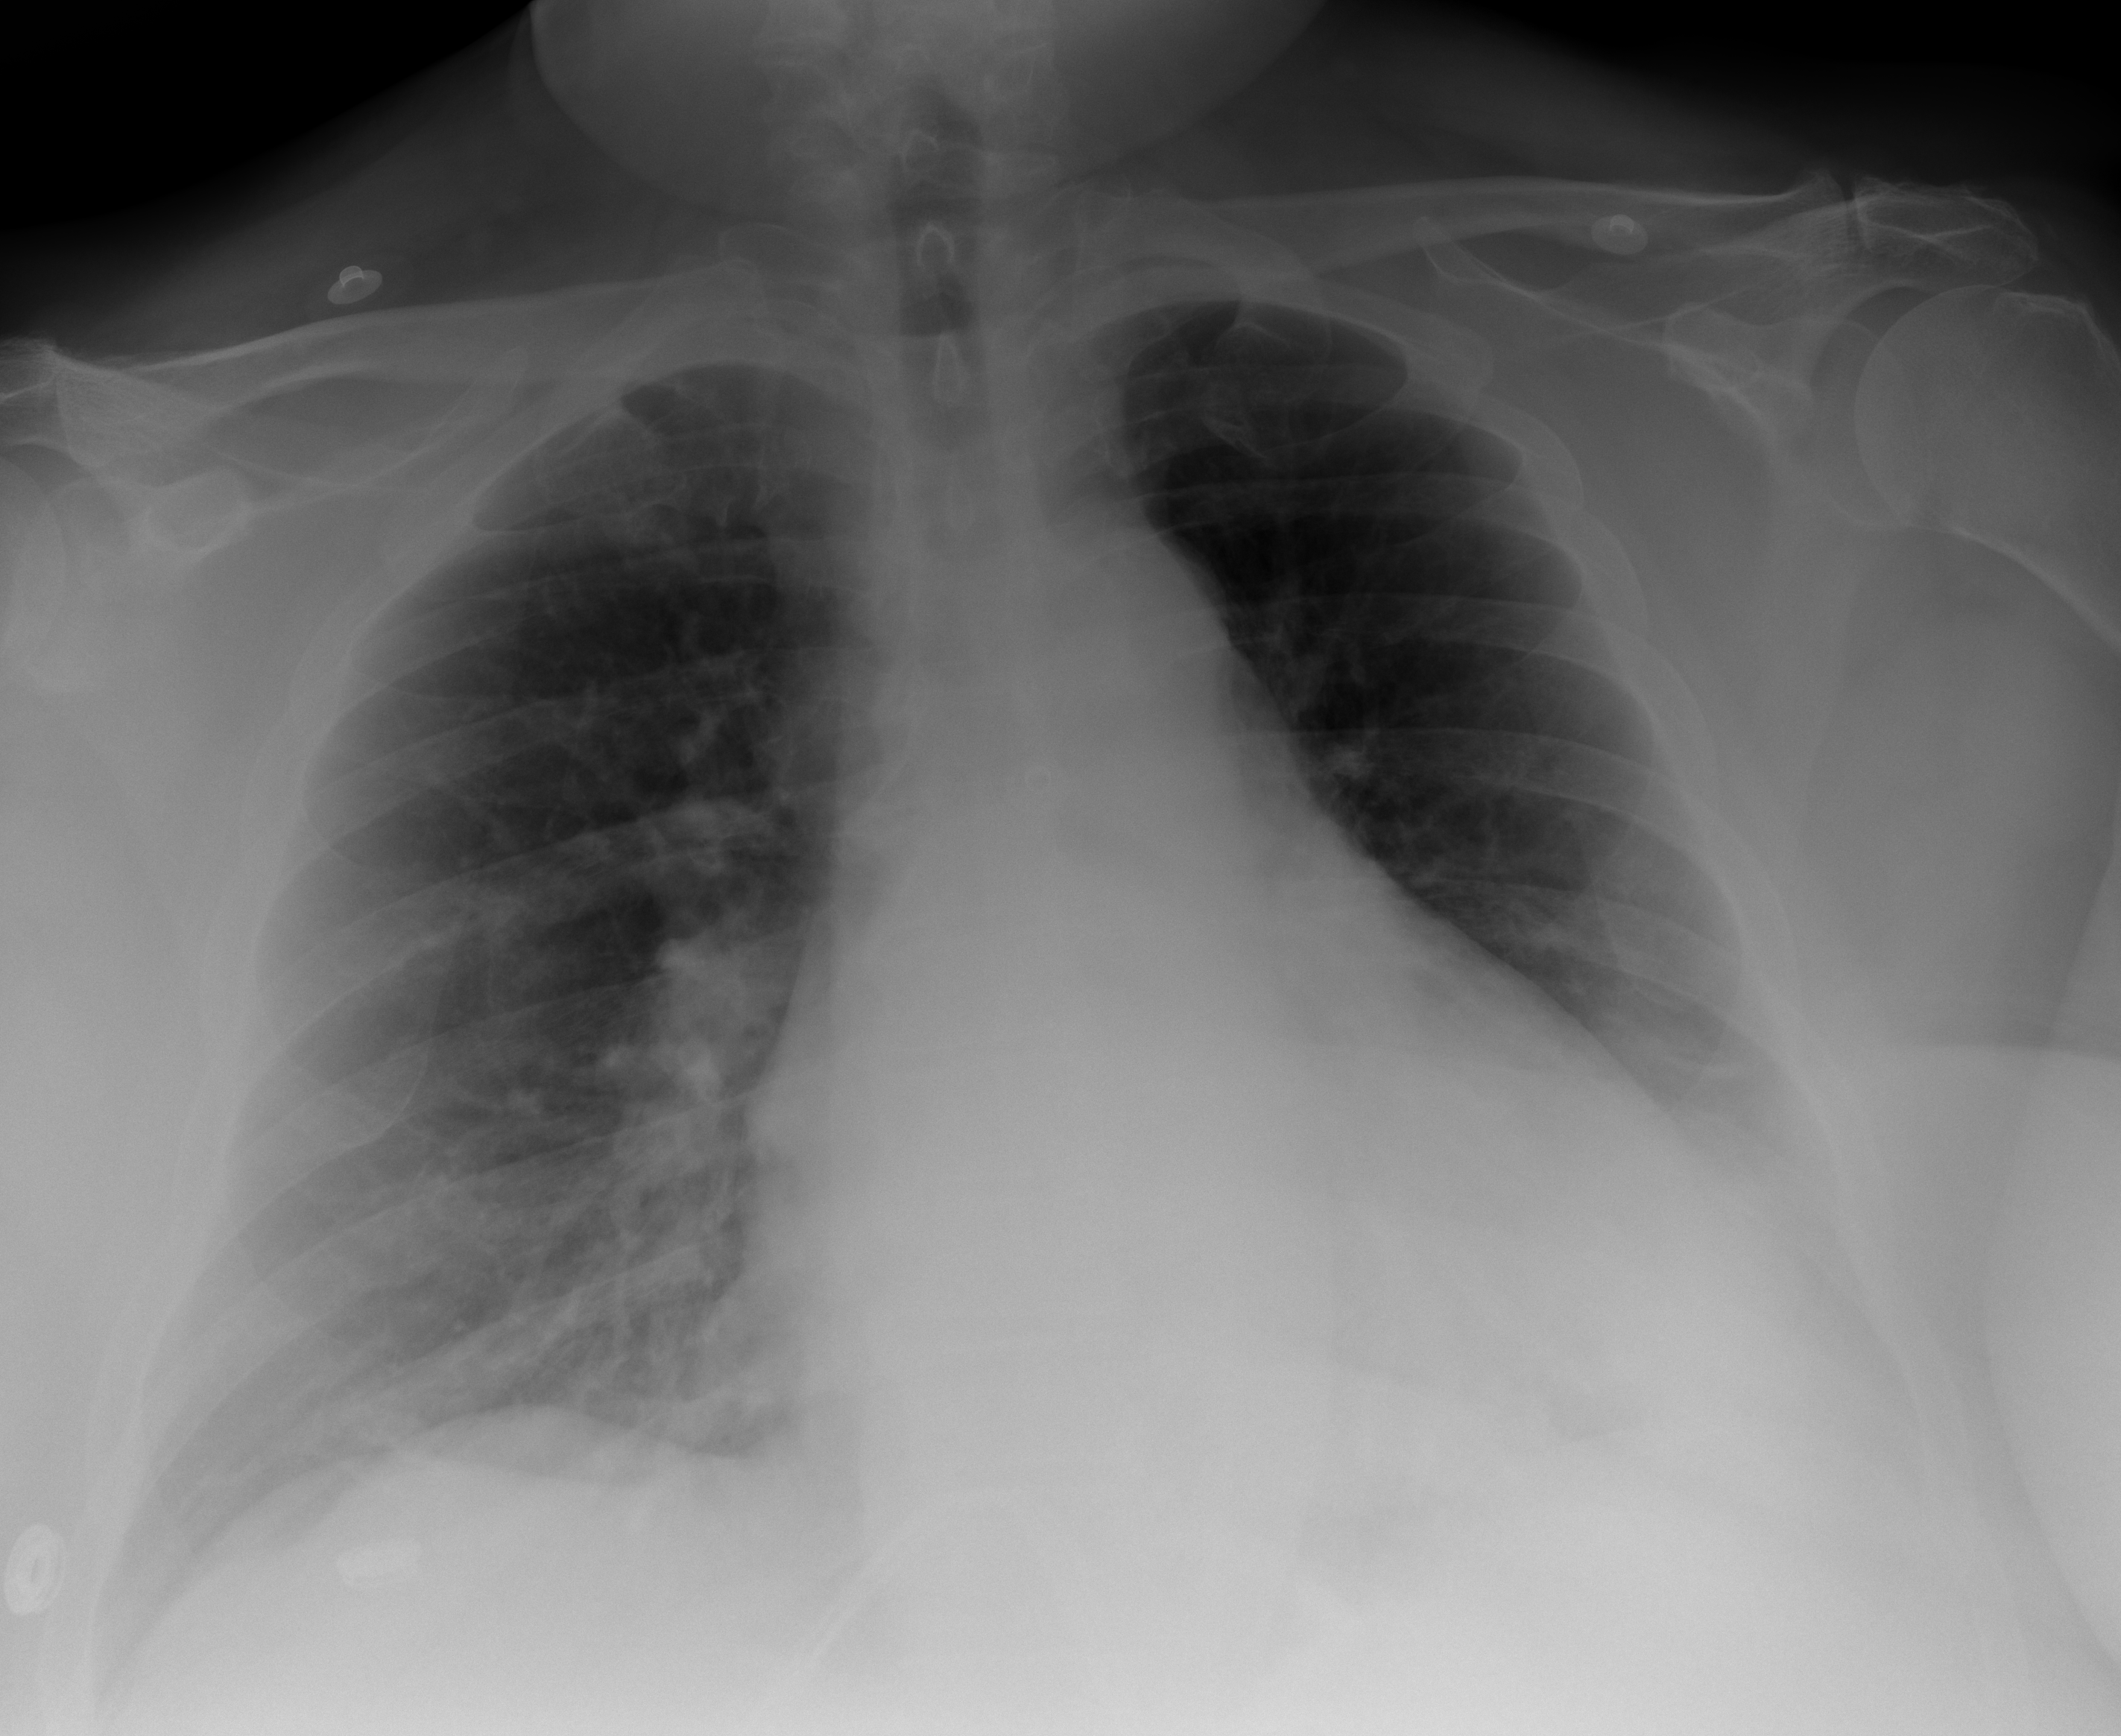
Chest X-ray (portable), AP projection. Female patient, age 59 years; imaged 1 day after the COVID-19 diagnosis.
Key findings recorded by the radiologist: Atelectatic changes are seen in the right lung base. On the left, there is diffuse haziness with partial obliteration of the left hemidiaphragm interface.